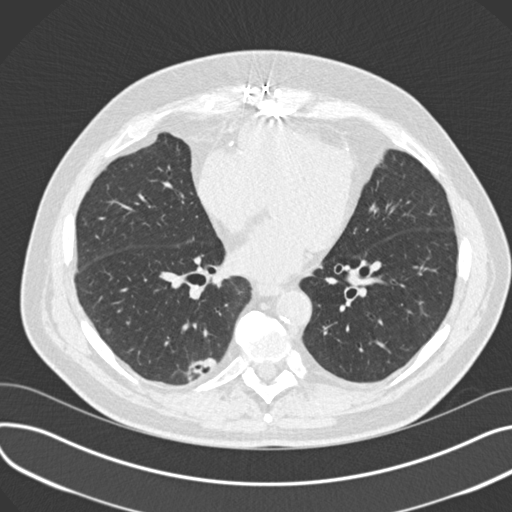
Axial slice from a low-dose chest CT screening exam. Third annual screen. Lung window (W 1500 / L -600 HU). 2 mm slice thickness. Standard (soft-tissue) reconstruction kernel (B30f). 120 kVp. Male participant, aged 68 years at enrolment.
Lesion marked by an expert reader, bounding box (x1, y1, x2, y2) in pixels: (177, 347, 221, 387). The screening reader recorded 4 non-calcified nodules or masses ≥4 mm on this exam (left upper lobe, lingula, right upper lobe, right lower lobe); which of them this box marks is not recorded. Later outcome: lung cancer diagnosed 68 days after this screen — adenosquamous carcinoma, right lower lobe, moderately differentiated (G2), stage IB (AJCC 6th edition), 31 mm at pathology.